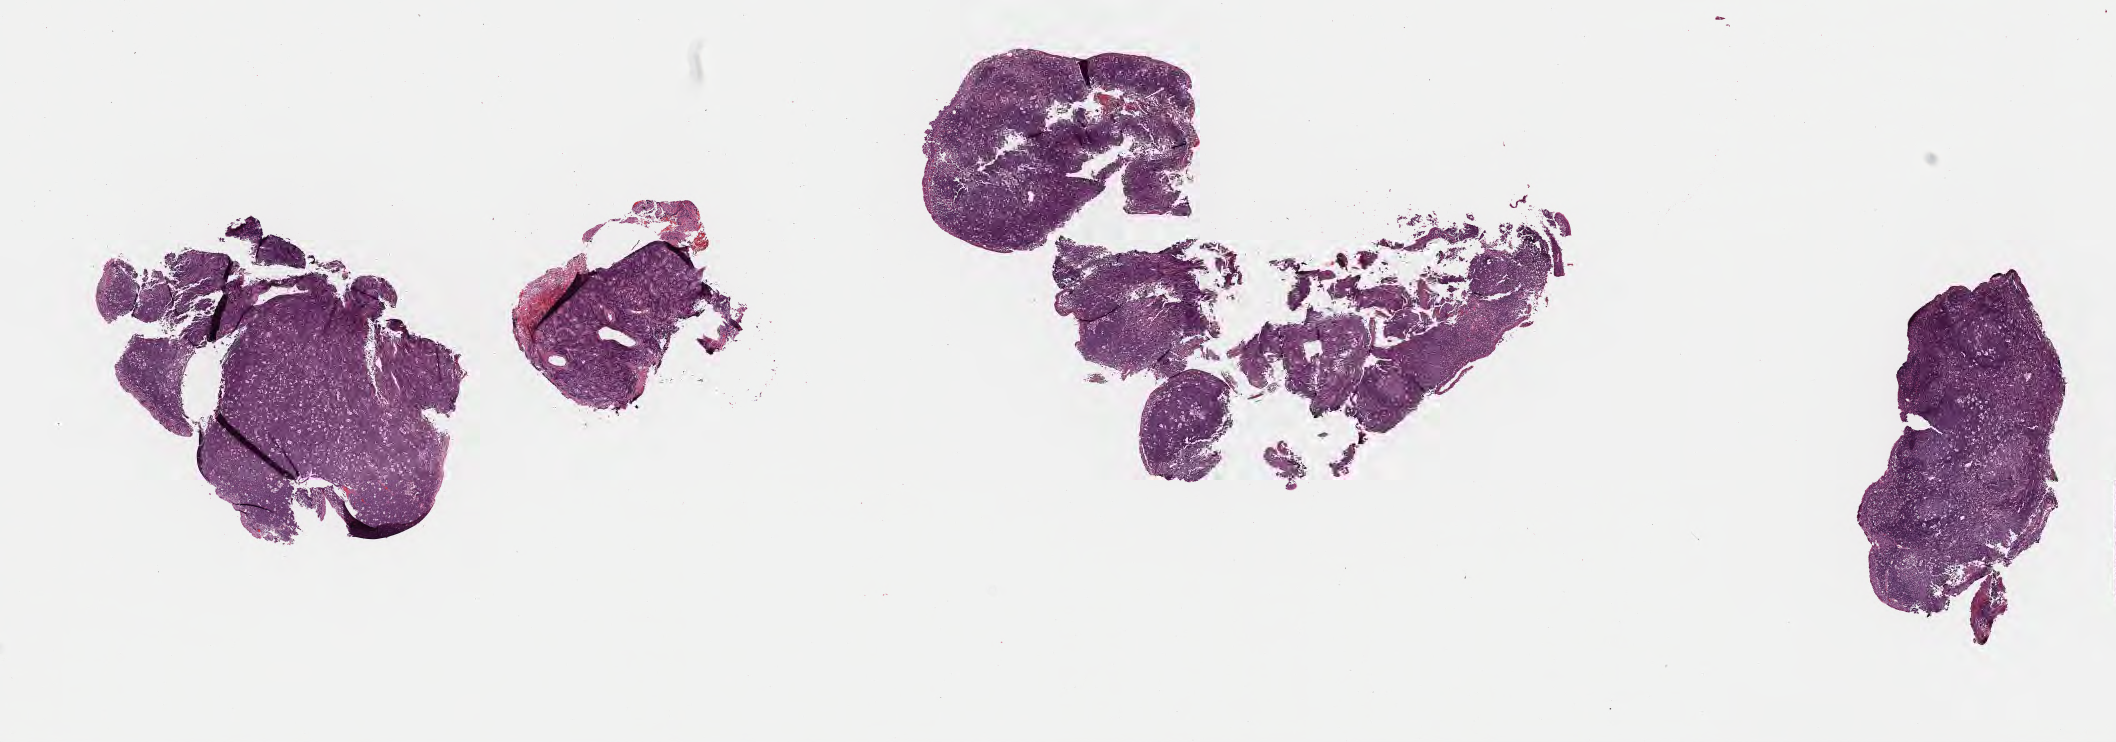
Whole-slide image, haematoxylin and eosin stain — a low-resolution overview of the entire scanned area, about 17.1 x 6.0 mm, FFPE section, primary tumor. Patient: male, age at initial diagnosis 5 years. Pathologist review of this section (percent, as recorded): tumor cells 85%, tumor nuclei 85%, stromal cells 10%, necrosis 0%, normal cells 5%. Infiltration values recorded for this section: lymphocyte infiltration 70%, monocyte infiltration 15%, neutrophil infiltration 5%.
Diagnosis: Burkitt lymphoma, NOS. Section: bottom of the tissue portion. Ann Arbor stage (patient): Stage IV.